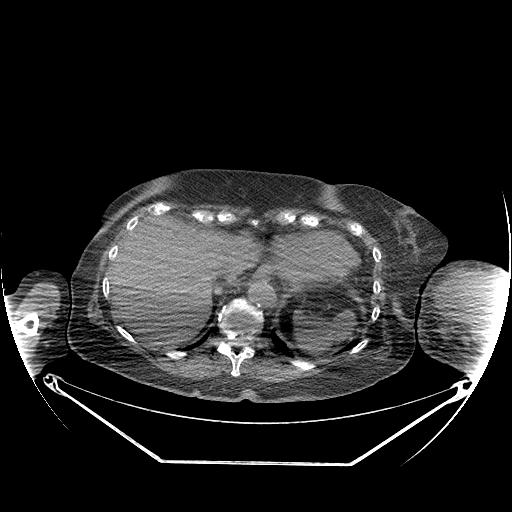
CT of an extremity soft-tissue mass (from a PET/CT study), one axial slice; position 140 of 267 along the scan axis; reconstruction kernel STANDARD; soft-tissue window (W 400 / L 40 HU); 3.75 mm slice thickness; 512 × 512 image matrix, field of view 500 × 500 mm. Female patient. From the clinical record (not read from this slice): histological type: pleiomorphic leiomyosarcoma; grade: high; site of the primary tumour: left biceps.
Annotated regions visible in this slice (expert contour drawn on MRI and transferred to this co-registered scan by the dataset authors):
- gross tumour volume including surrounding oedema: bounding box (x1, y1, x2, y2) in pixels: (470, 290, 501, 320)
- gross tumour volume (mass): (475, 290, 487, 300)